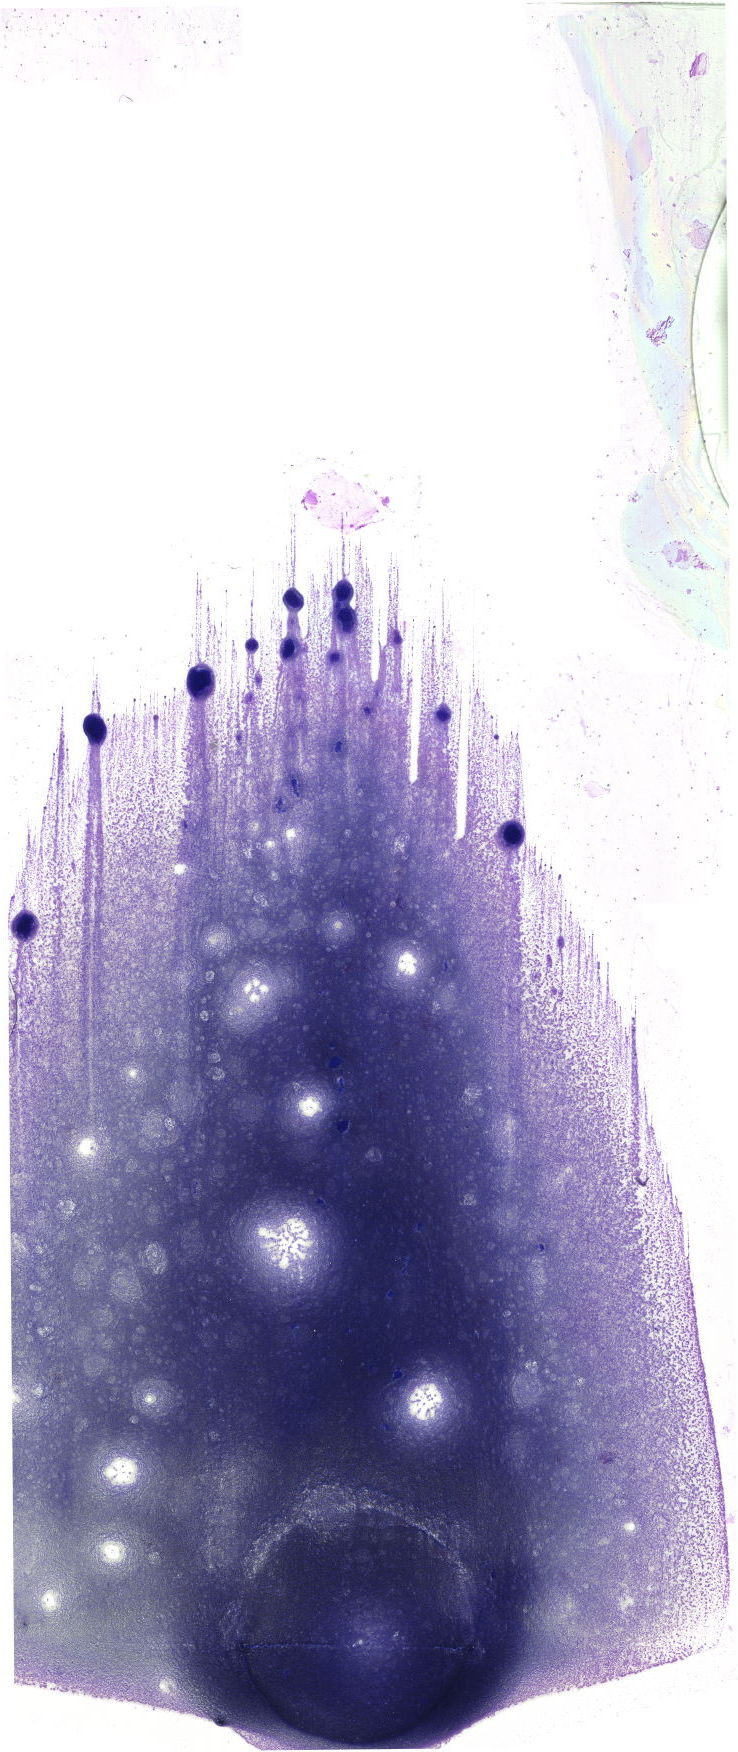
Bone marrow aspirate smear, May-Grünwald–Giemsa stain, whole-slide image — shown as a low-resolution overview of the whole scanned area (about 20.9 x 49.7 mm). Patient sex: female.
• diagnosis: Chronic Phase Chronic Myeloid Leukemia, BCR-ABL1 Positive